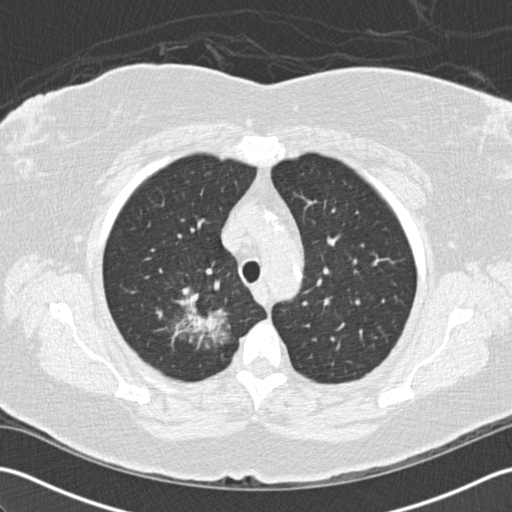
Low-dose screening chest CT, axial slice; first (baseline) screen; lung window (W 1500 / L -600 HU); 2 mm slice thickness; standard (soft-tissue) reconstruction kernel (B30f); slice 32 of 156 in the series; 512 × 512 image matrix. Female, age 72 years at enrolment. Former smoker at enrolment.
Expert reader's lesion annotation, bounding box (x1, y1, x2, y2) in pixels: (138, 274, 236, 368). The screening reader recorded 2 non-calcified nodules or masses ≥4 mm on this exam; which of them this box marks is not recorded. Official screen result: positive, change unspecified: nodule(s) >= 4 mm or enlarging nodule(s), mass(es), or other non-specific abnormalities suspicious for lung cancer.